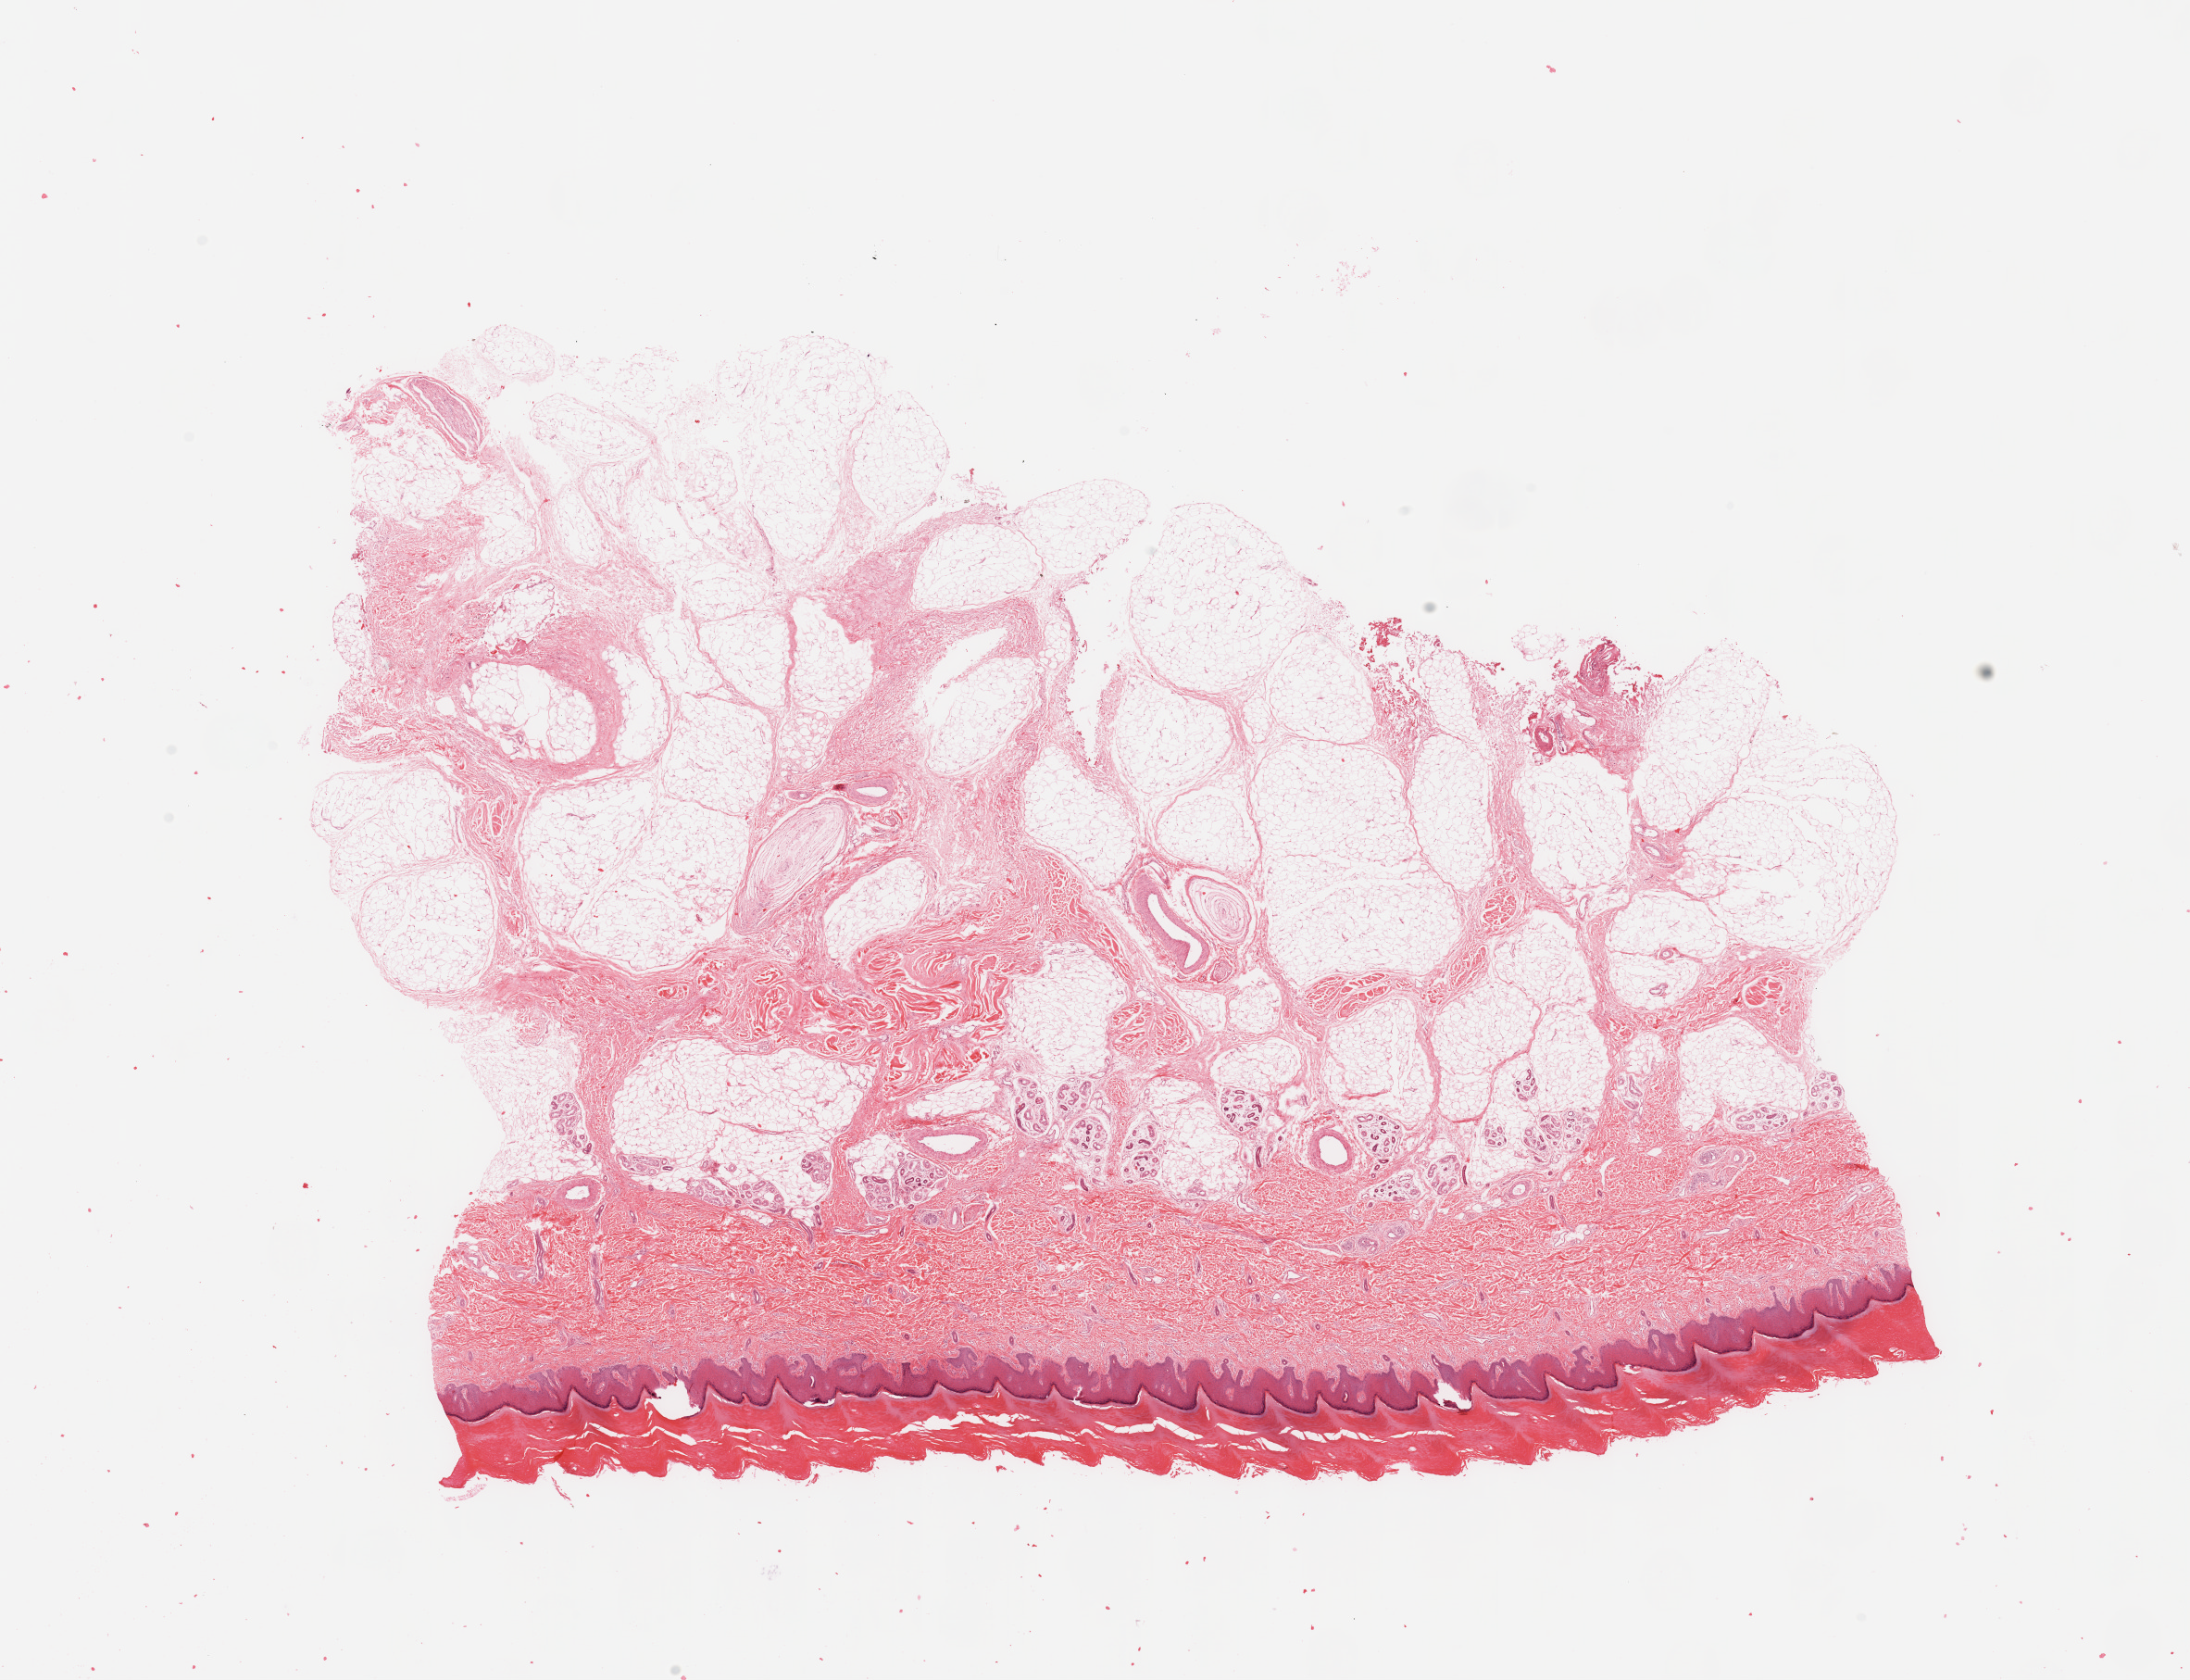
H&E-stained whole-slide image — a low-resolution overview of the entire scanned area, about 18.7 x 14.3 mm (from a 20x scan). Normal (non-tumour) tissue sample, sampled site: lymph node. Male, 69 y/o.
This section: normal (non-tumour) tissue from the same patient. Patient diagnosis: Malignant melanoma, NOS.